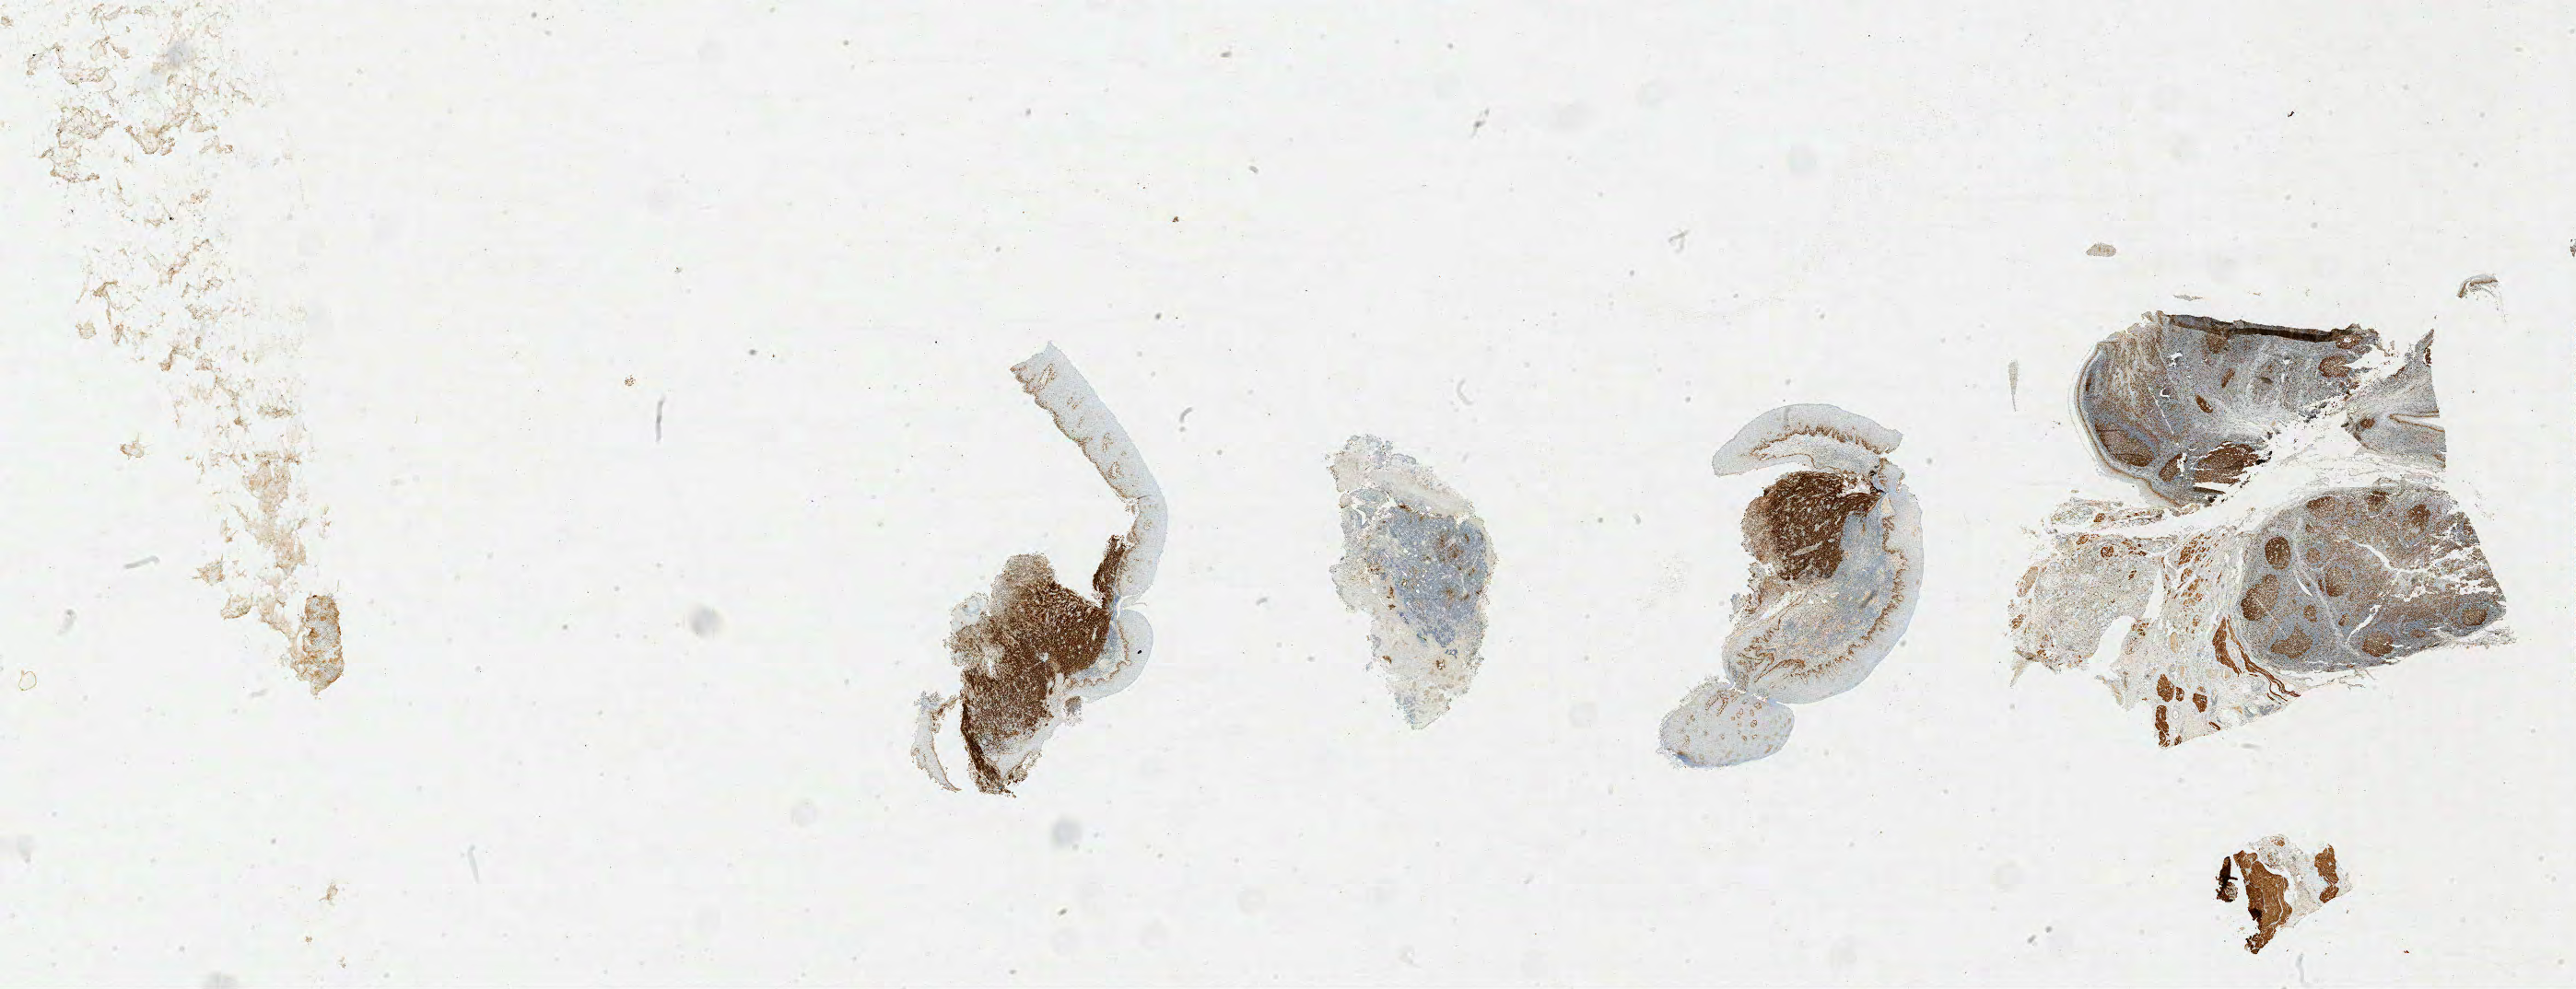
Whole-slide image, immunohistochemical stain for Ki-67, shown as a low-resolution overview of the whole scanned area (about 44.6 x 17.1 mm). Specimen: tumor tissue. Male patient, age 66 years.
Histologic diagnosis: Burkitt lymphoma, NOS.